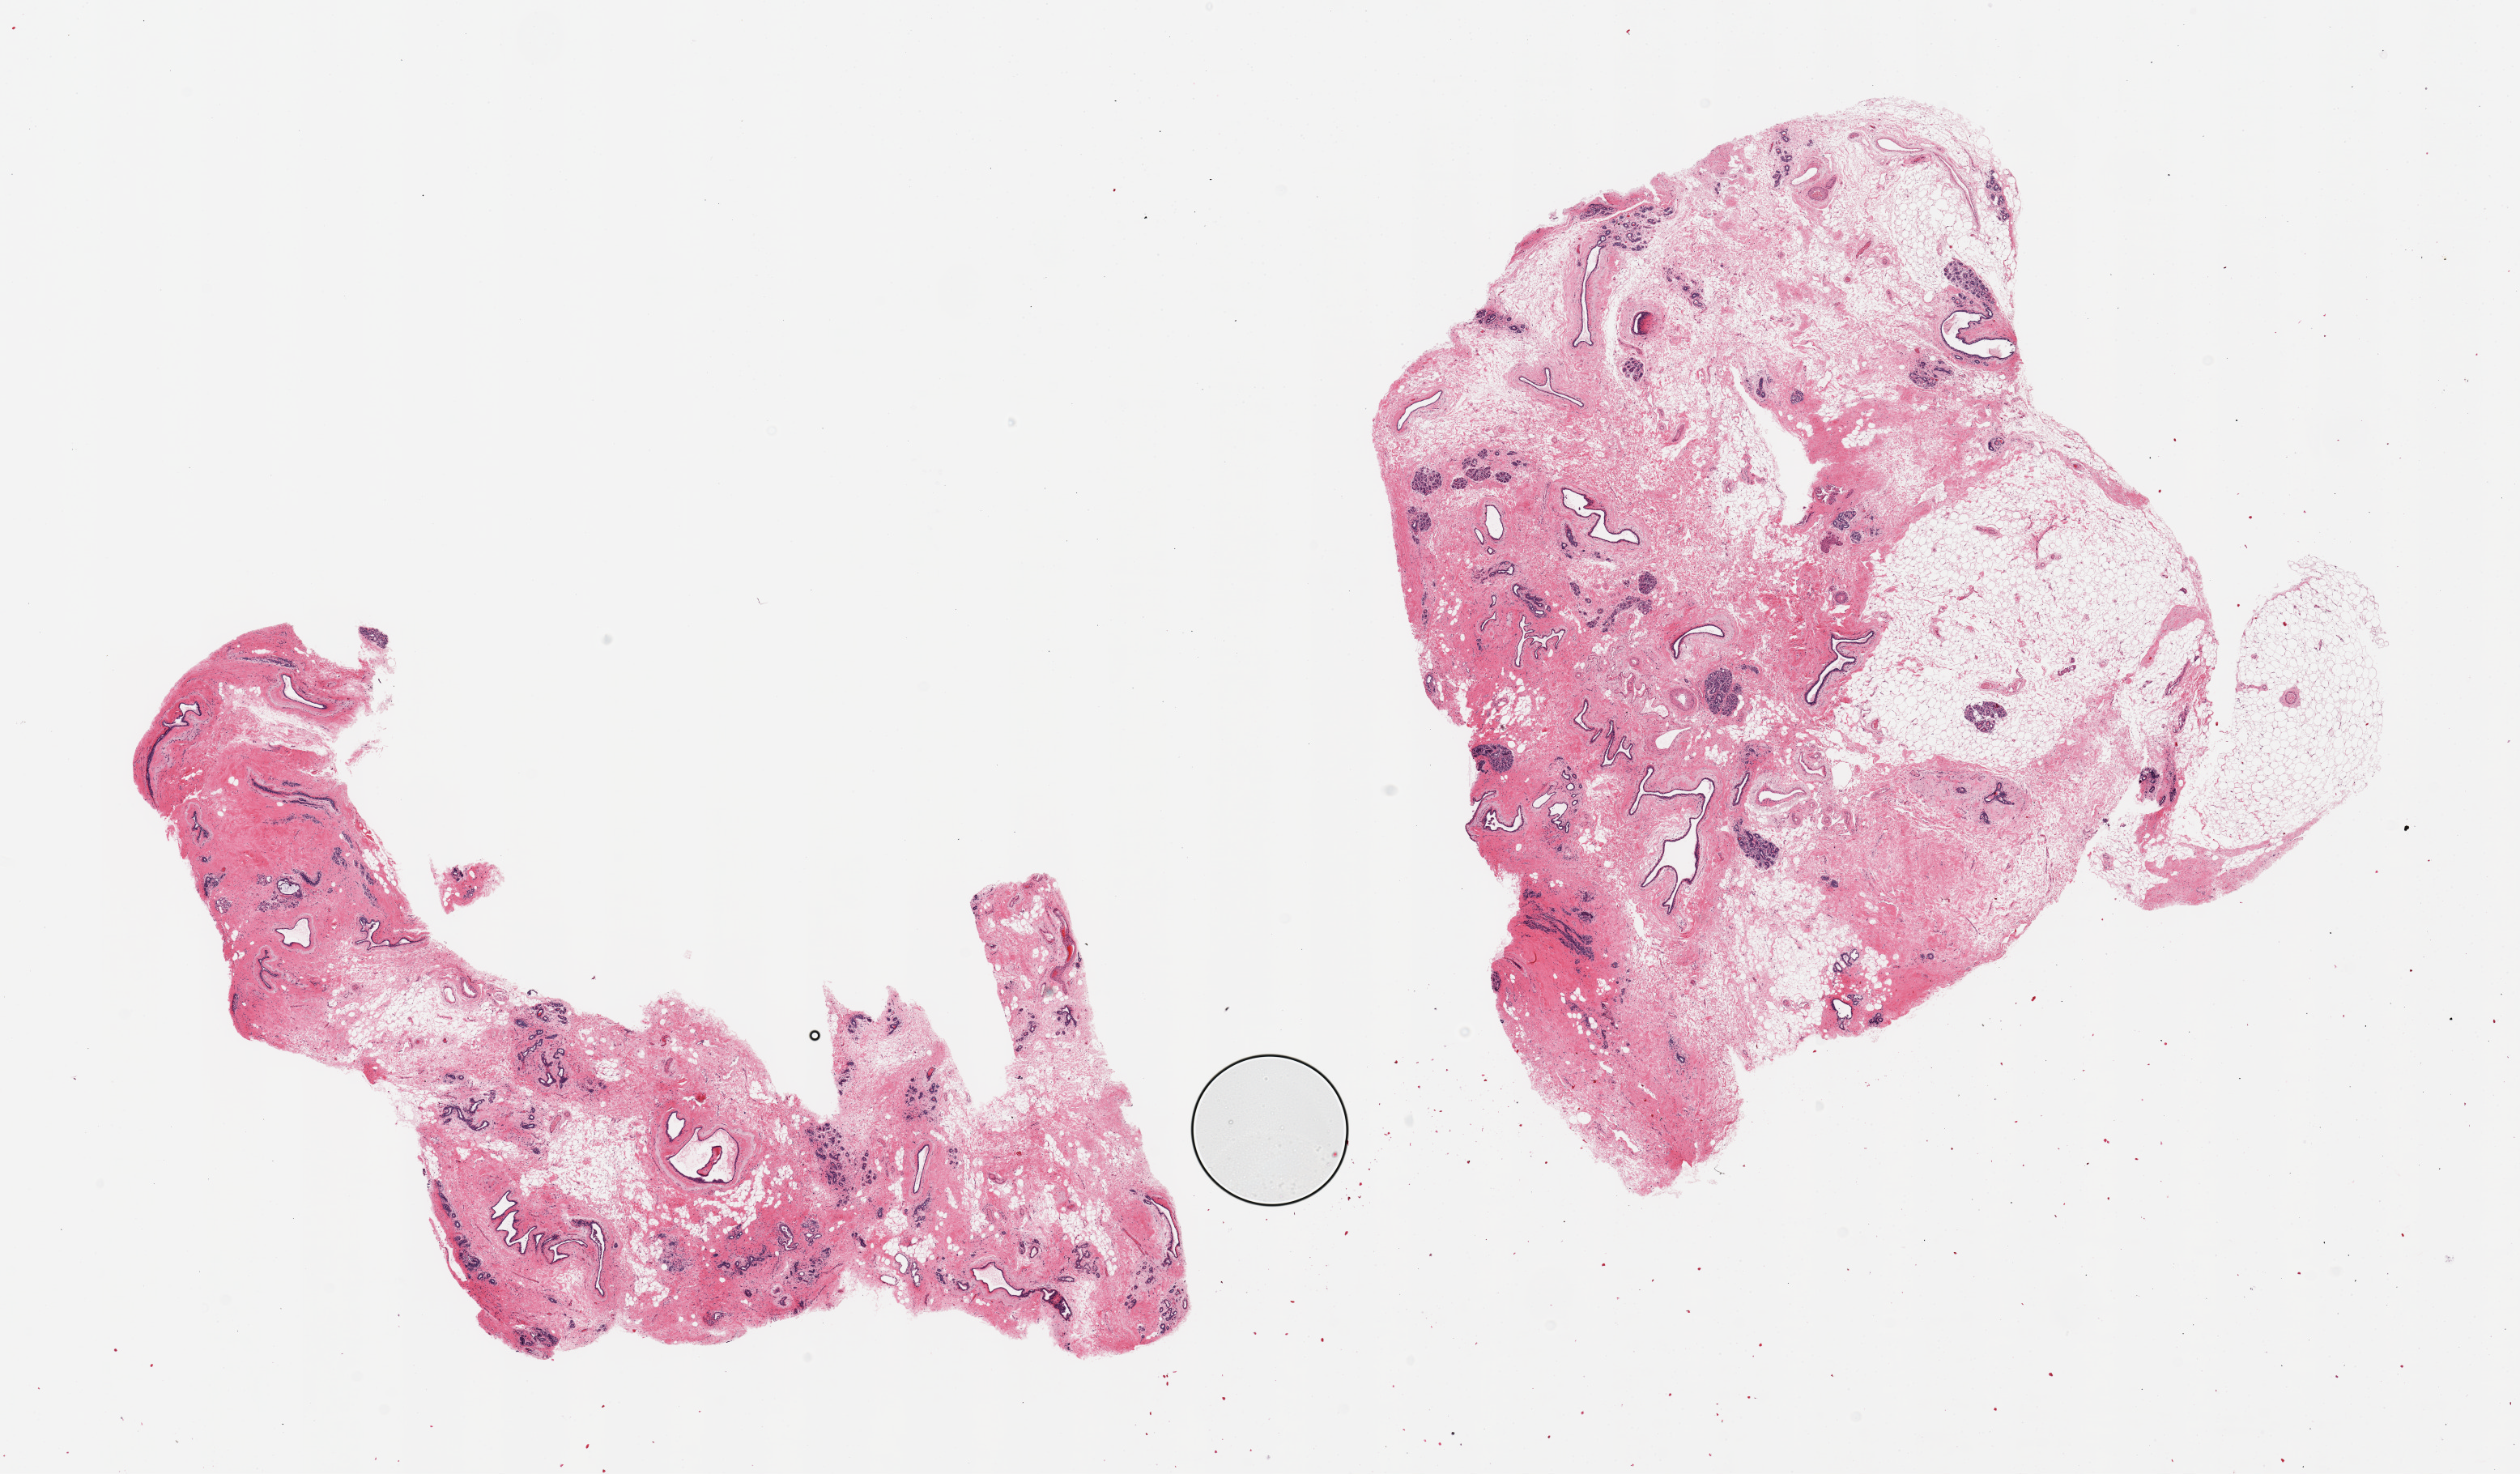
Hematoxylin and eosin (H&E) whole-slide image — whole scanned area (about 24.6 x 14.4 mm, acquisition: 20x scan) shown as a low-resolution overview. PAXgene-fixed paraffin-embedded (PFPE) section. Target tissue: breast. Tissue donor sample. Female donor.
- reviewer comment on this tissue sample: 2 pieces; fibroadipose tissue, small lobules and ducts embedded in fibrotic stroma